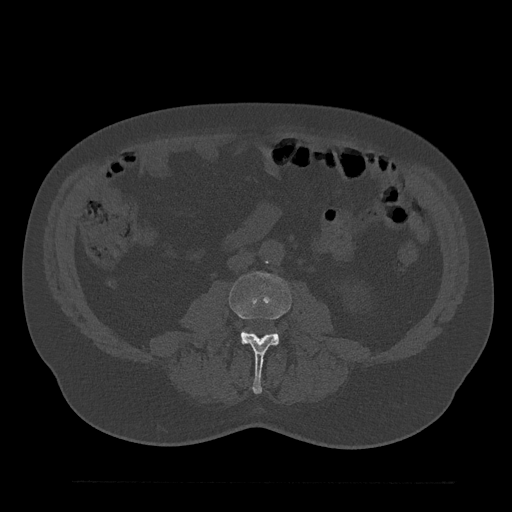
CT including the spine, one axial slice; position 19 of 797 along the scan axis; reconstruction kernel Br40s/3; bone window (W 1800 / L 400 HU); 0.5 mm slice thickness; 512 × 512 image matrix, field of view 430 × 430 mm. Patient: male, 61 years. Case-level facts recorded for this patient, not image findings: primary cancer: prostate.
Annotated regions visible in this slice (semi-automatic segmentation, software-assisted and operator-edited):
- L3 vertebra: bounding box [x1, y1, x2, y2] px = [229, 272, 291, 394]